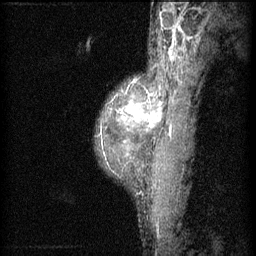
Breast MRI (dynamic contrast-enhanced), one sagittal slice; position 46 of 60 along the scan axis; 3 images stored at this slice position (order not interpretable as contrast timing); 1.5 T; TE 4.2 ms, TR 11 ms; 2 mm slice thickness; 256 × 256 image matrix, field of view 180 × 180 mm. Patient: female, 40 years.
Annotated regions visible in this slice (semi-automatic segmentation, software-assisted and operator-edited):
- analysis volume of interest (the breast-tissue region the enhancement analysis was run in; not a lesion): bounding box [x1, y1, x2, y2] px = [100, 42, 177, 199]
- tumour enhancement mask (voxels above the 70 % enhancement threshold inside the analysis volume of interest): [122, 100, 161, 127]